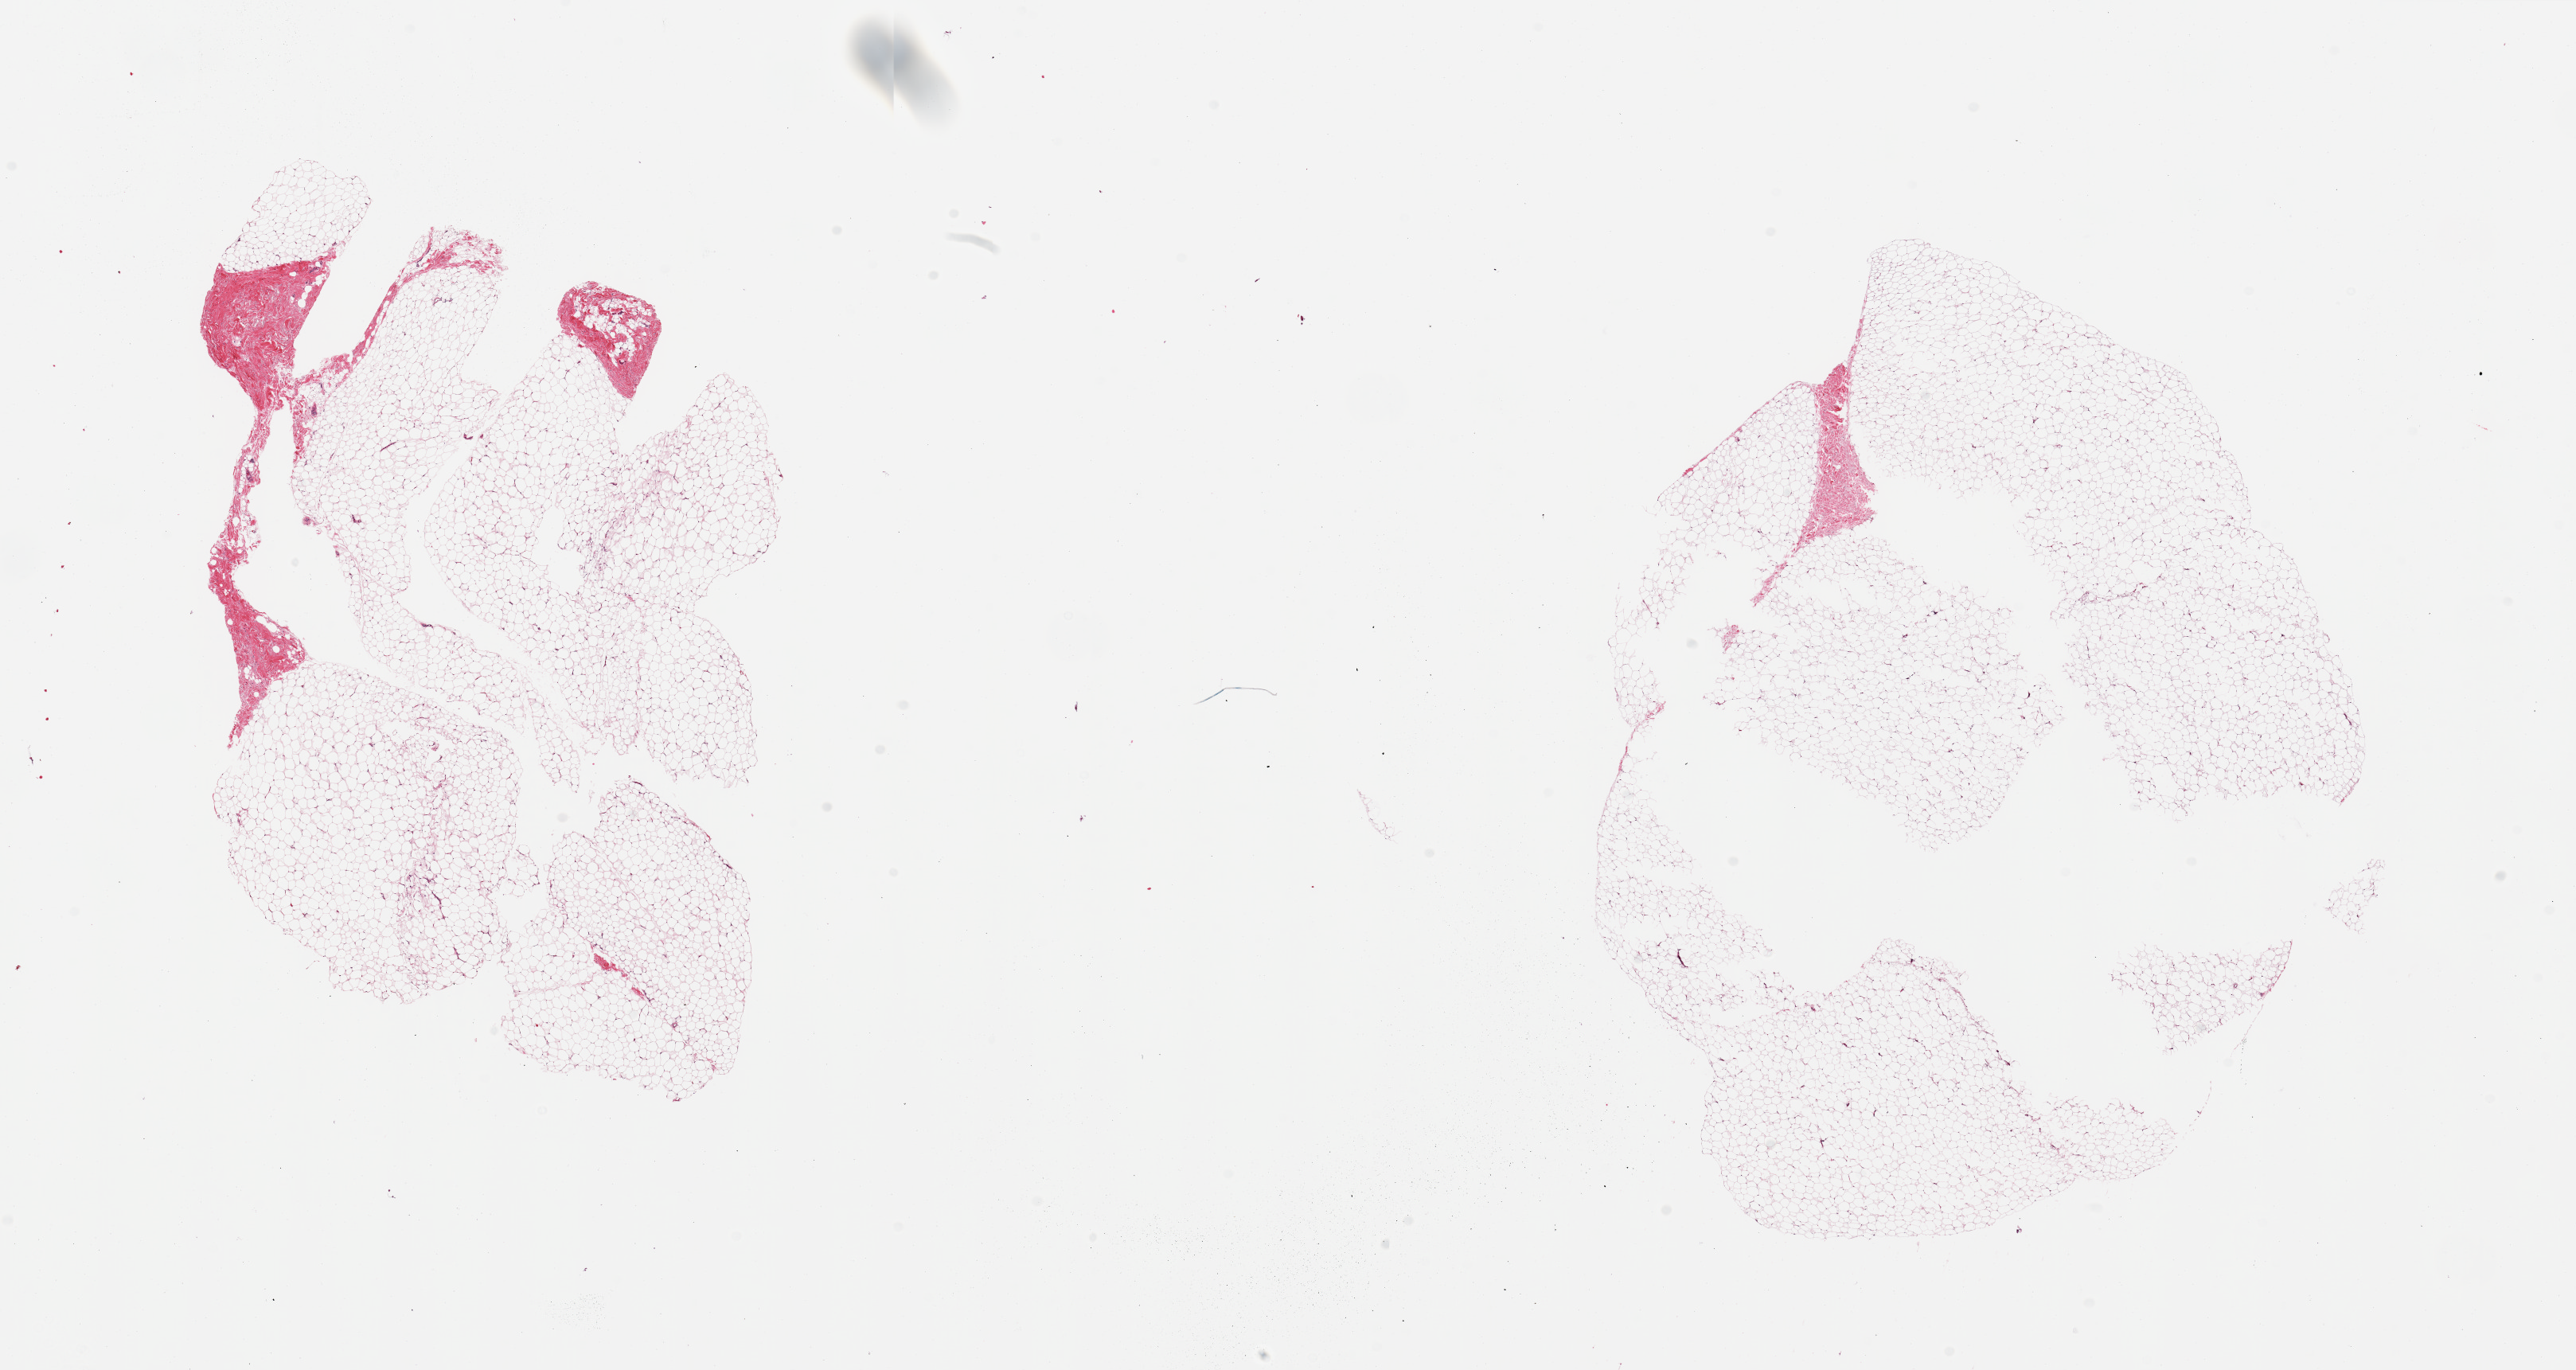
Digitized haematoxylin and eosin-stained section — low-resolution overview of the scanned area, about 25.6 x 13.6 mm. PAXgene-fixed paraffin-embedded (PFPE) section. Target tissue: breast. Tissue donor sample.
Pathologist's review note for this sample: 2 pieces, fibroadipose elements only, no ductal elements.